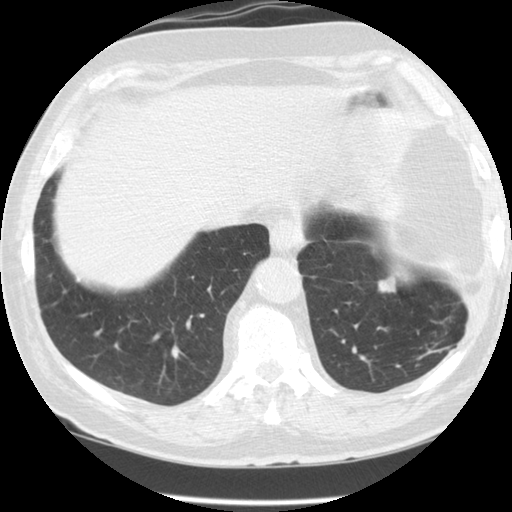
Low-dose screening chest CT, one axial slice. Position 32 of 127 along the scan axis. Reconstruction kernel STANDARD. 120 kVp. Lung window (W 1500 / L -600 HU). 2.5 mm slice thickness. 512 × 512 image matrix, field of view 340 × 340 mm.
Structures marked on this image (expert manual segmentation):
- lesion 1 (tumor, lower lobe of left lung): bounding box <379,275,396,292> (left, top, right, bottom; pixels)